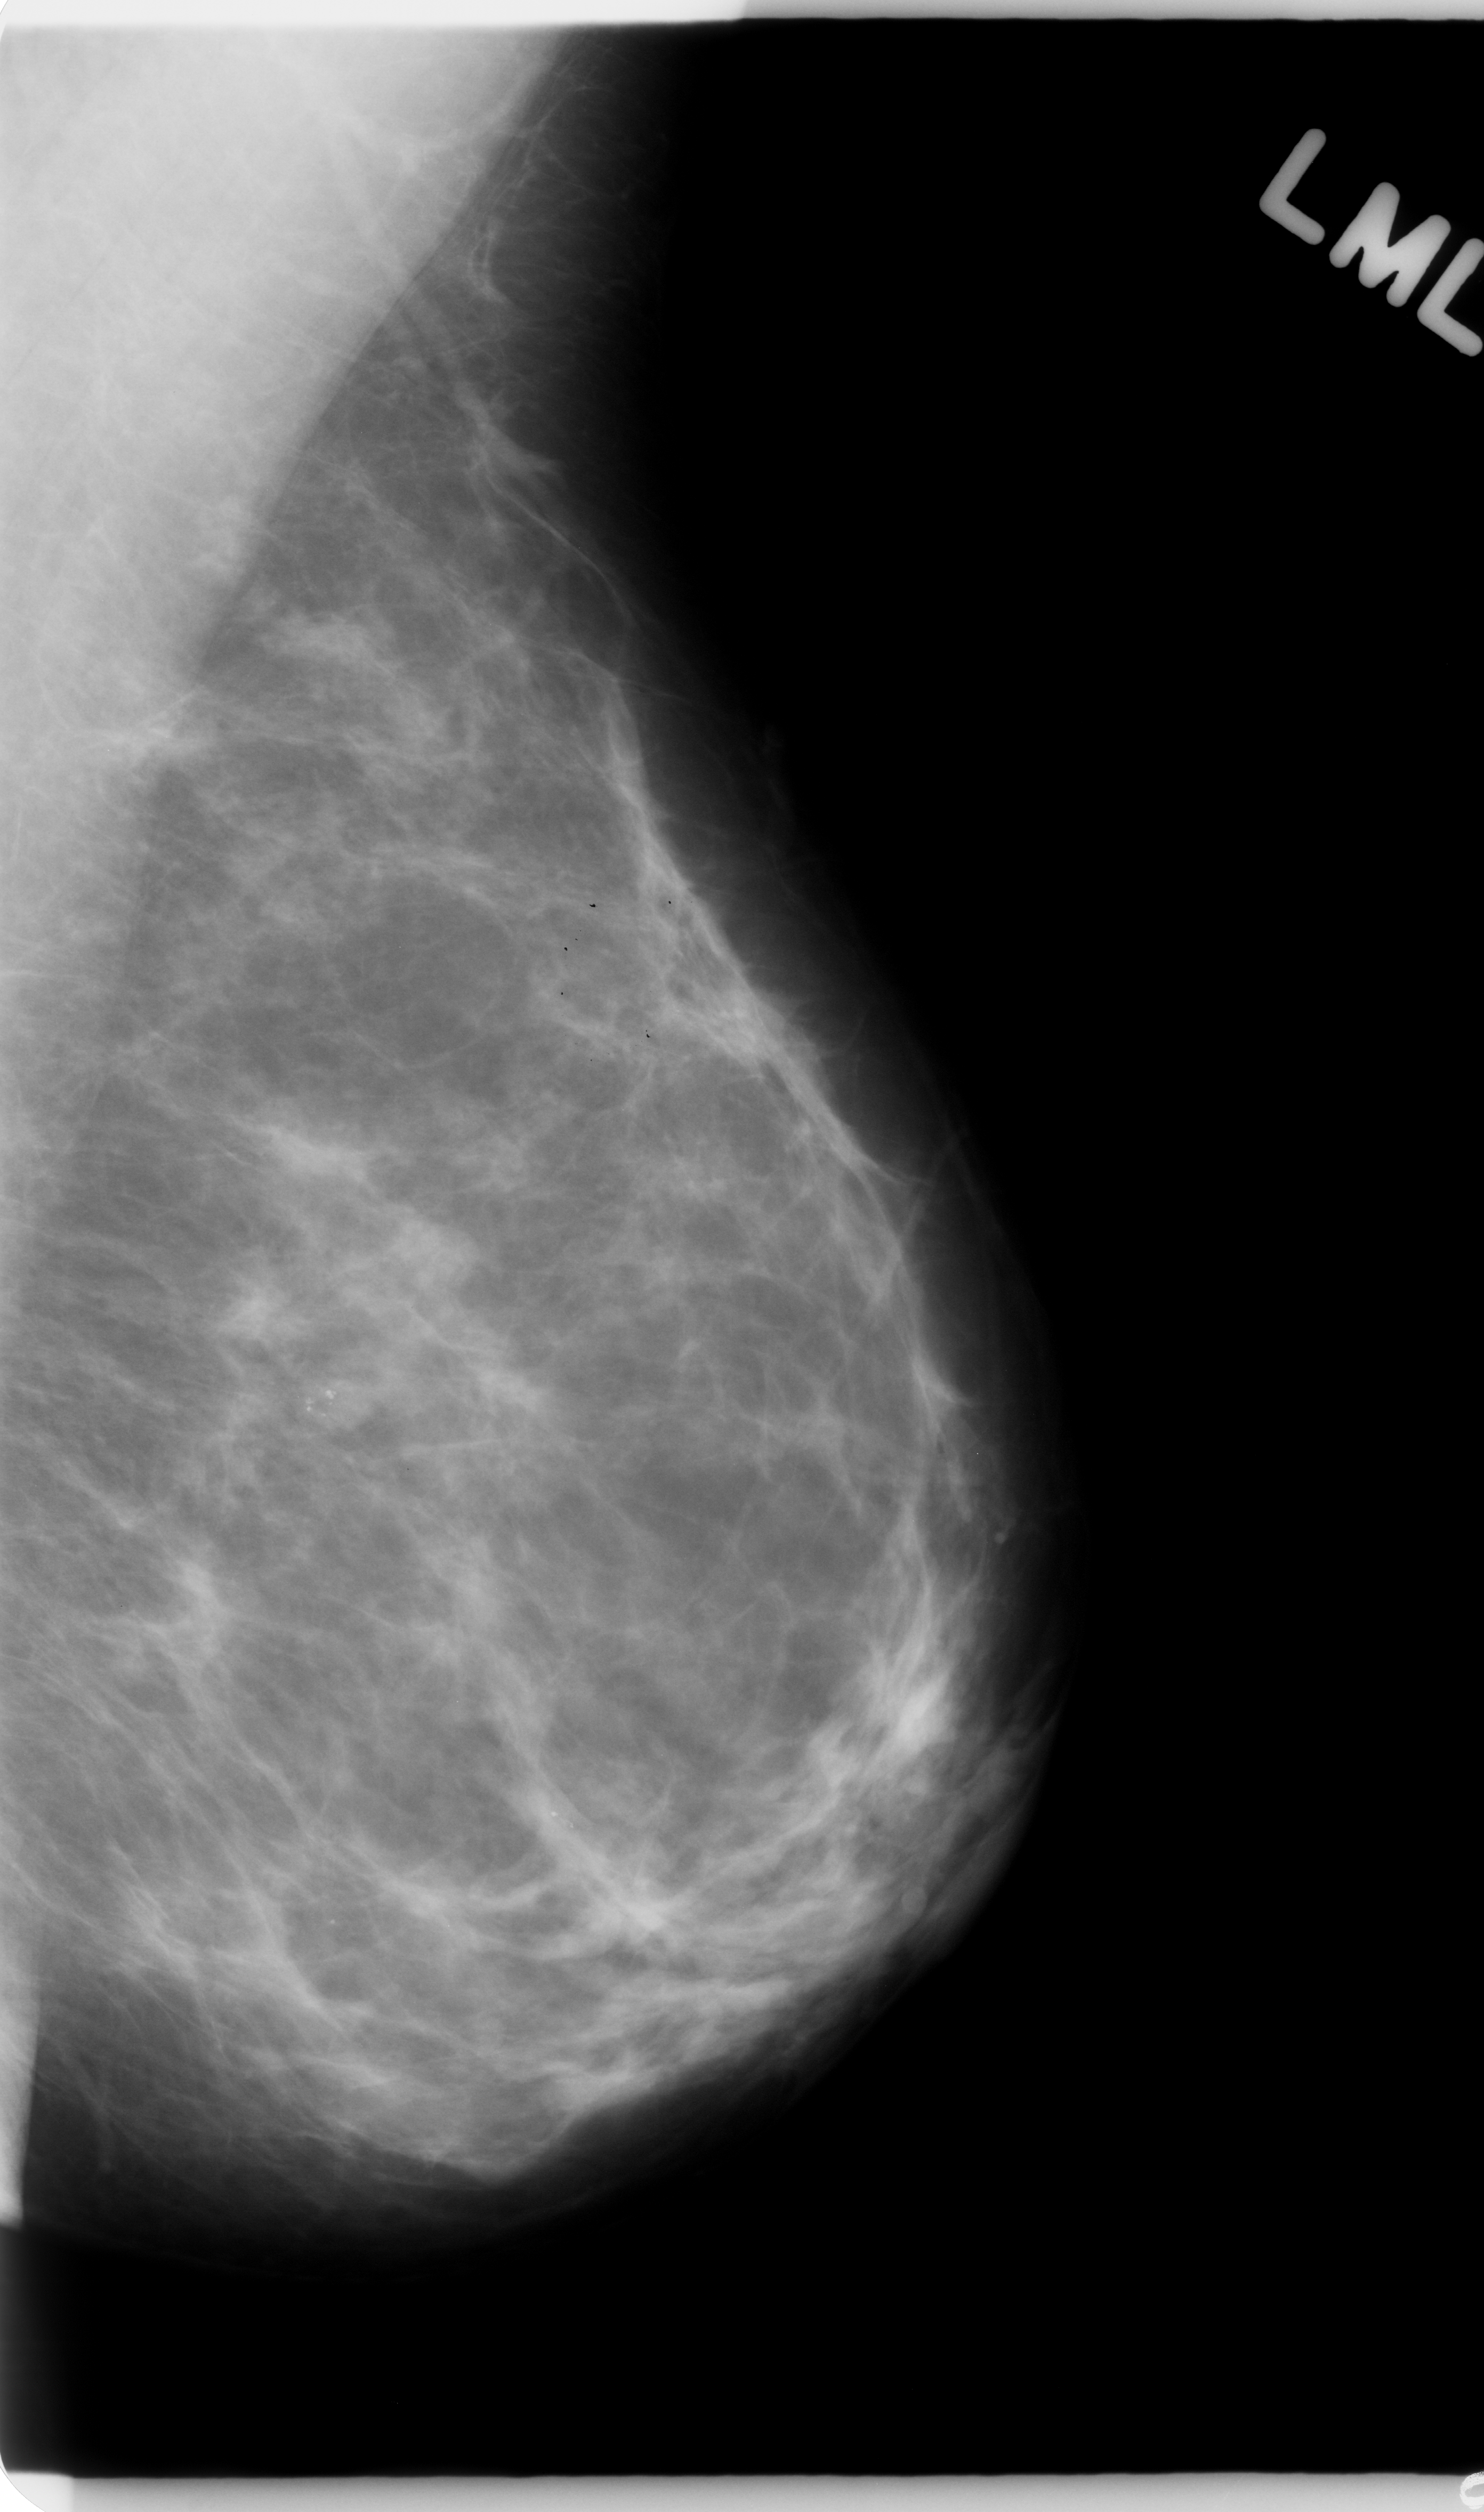
Scanned film-screen mammogram; left breast; mediolateral oblique (MLO) view; BI-RADS breast density category 2 (scale 1–4).
Abnormality record for this image: Finding 1 of 2: calcifications, morphology punctate, distribution clustered; BI-RADS assessment category 3; pathology (as recorded): benign. Finding 2 of 2: calcifications, morphology punctate, distribution clustered; BI-RADS assessment category 4; subtlety rating 5 on a 1 (subtle) to 5 (obvious) scale; pathology (as recorded): benign.